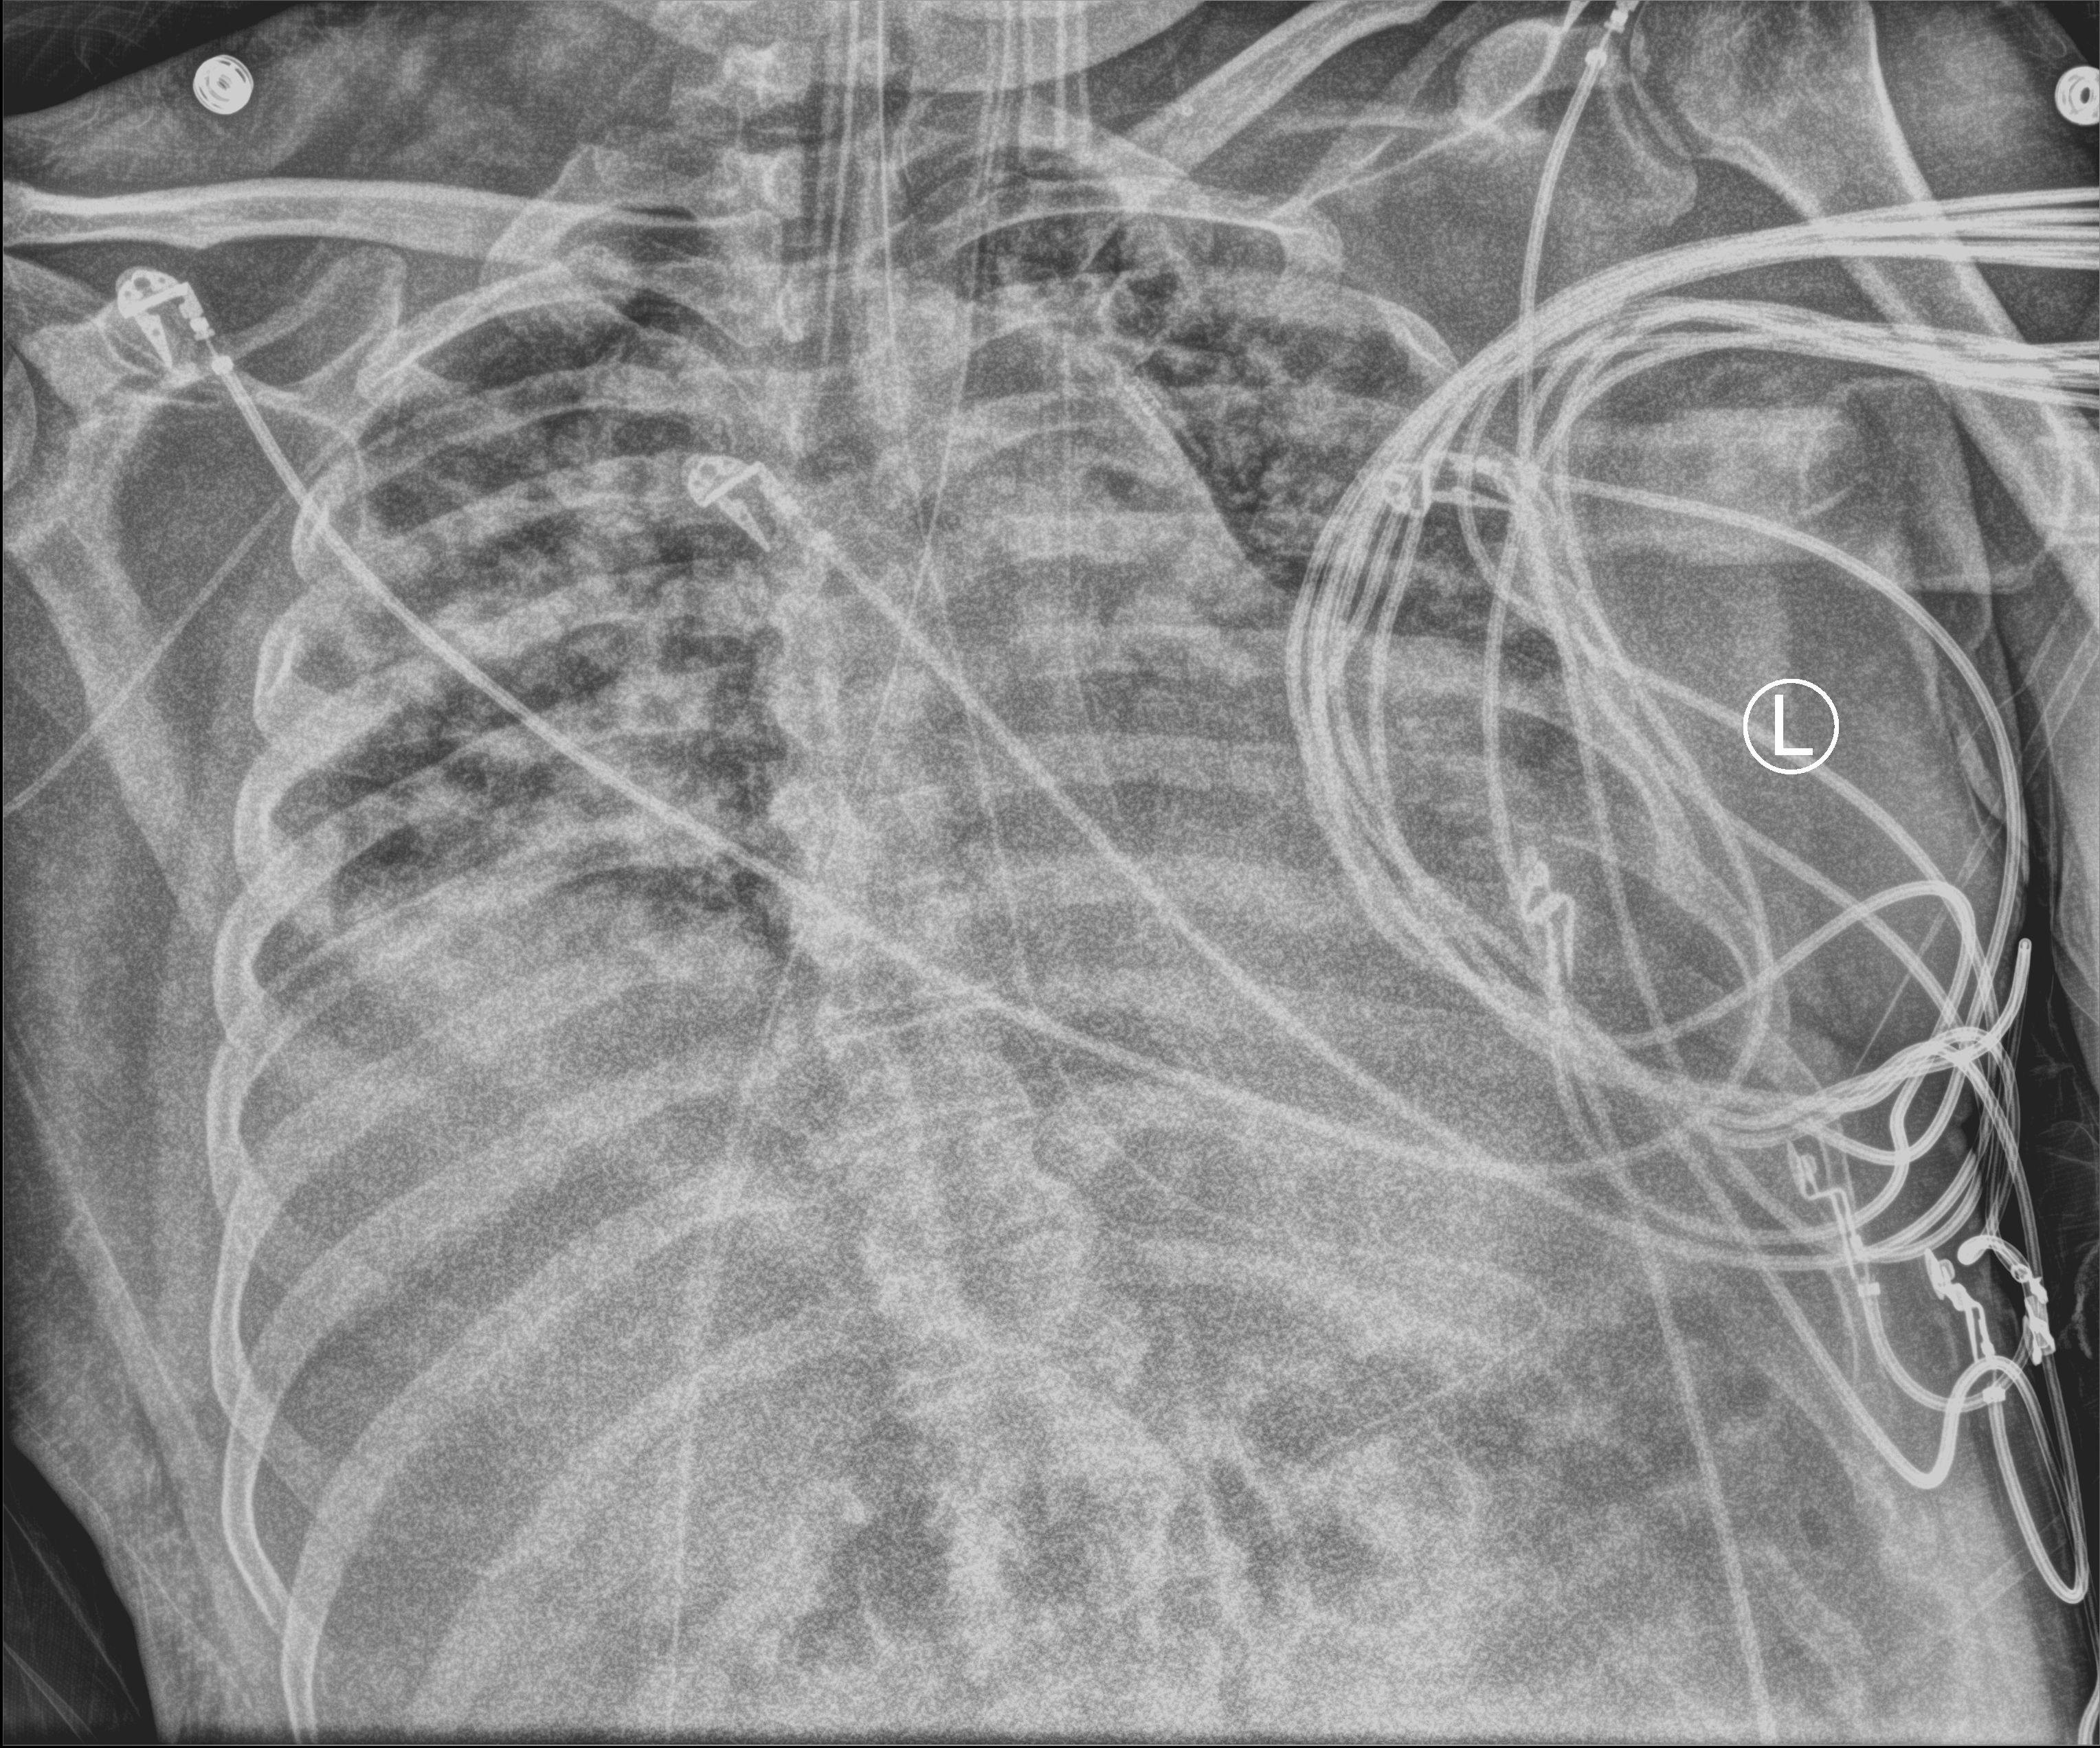
Portable chest radiograph; anteroposterior (AP) projection. Patient hospitalised with COVID-19; male, aged 18–59 years.
Hospital-stay facts (about this admission, not read from this image; timing relative to this image not recorded): length of hospital stay: 26 days.